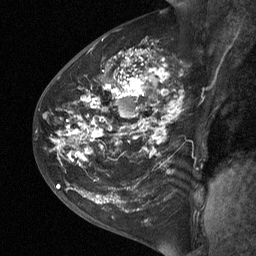
Breast MRI (dynamic contrast-enhanced), one sagittal slice. Position 33 of 64 along the scan axis. Dynamic contrast-enhanced study with each time point stored as its own series, time point 2 of 3 at this slice position (early post-contrast, ordered by acquisition time). 1.5 T. TE 4.8 ms, TR 27 ms. 2 mm slice thickness. 256 × 256 image matrix, field of view 200 × 200 mm. Patient: female, 42 years. Case-level facts recorded for this patient, not image findings: setting: breast cancer imaged before/during neoadjuvant chemotherapy; receptor status: triple-negative.
Structures marked on this image (semi-automatically segmented with operator editing):
- analysis volume of interest (the breast-tissue region the enhancement analysis was run in; not a lesion): bounding box [x1, y1, x2, y2] px = [43, 29, 197, 190]
- tumour enhancement mask (voxels above the 90 % enhancement threshold inside the analysis volume of interest): [55, 50, 182, 161]